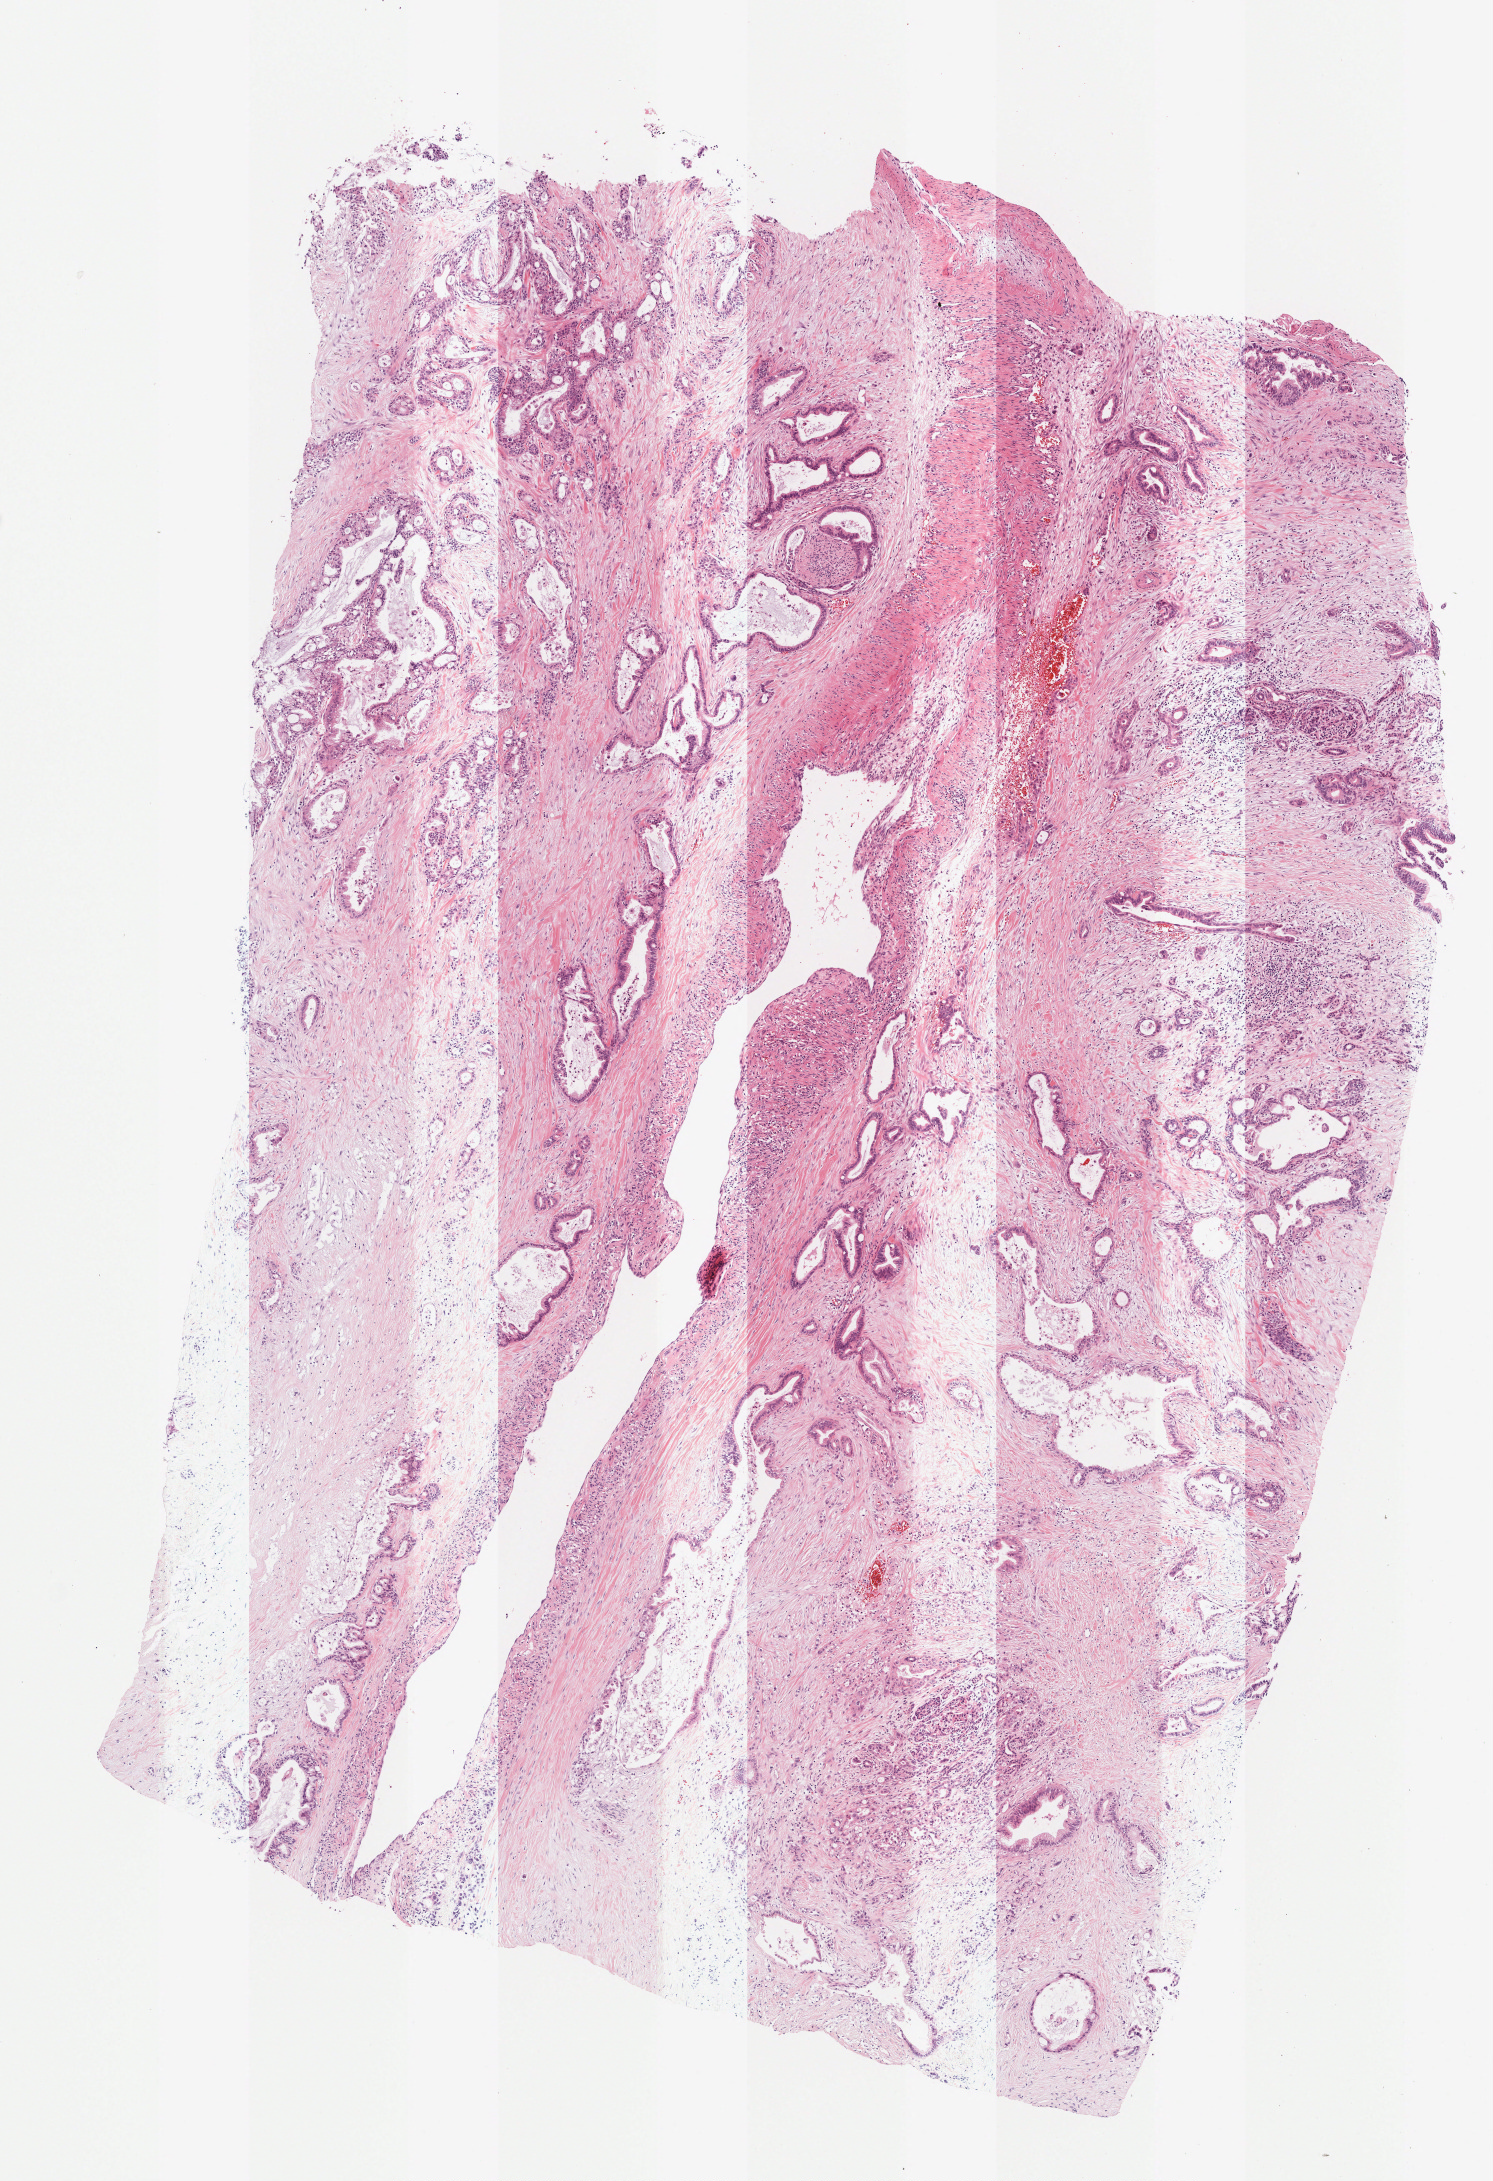
Whole-slide histology image, H&E — low-resolution overview of the scanned area, about 5.9 x 8.6 mm; frozen section from the top of the tissue portion; sample: primary tumour, pancreas. Male patient; age at initial diagnosis 50 years. Histologic grade: G2 (moderately differentiated). Slide review estimates, as recorded: tumour cells 80%, tumour nuclei 65%, normal cells 20%, stromal cells 0%, necrosis 0%. Infiltration values recorded for this section: lymphocyte infiltration 5%, monocyte infiltration 0%, neutrophil infiltration 0%.
• diagnosis: Infiltrating duct carcinoma, NOS (body of pancreas)
• lymph nodes positive (case pathology): 5 of 25 examined
• AJCC pathologic stage: IIA (7th edition)